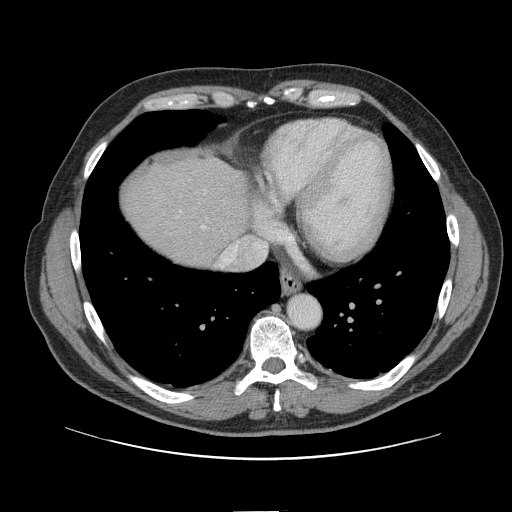
Contrast-enhanced abdominal CT, one axial slice; slice 136 of 161 in the series (ordered by position); 120 kVp; intravenous contrast given; soft-tissue window (W 400 / L 40 HU); 2.5 mm slice thickness; 512 × 512 image matrix. Male patient, age 66 years. Case-level facts recorded for this patient, not image findings: diagnosis: colorectal cancer liver metastases, imaged before liver resection; multiple liver metastases: no; largest metastasis: 3.5 cm; disease in both lobes: no.
Annotated regions visible in this slice (expert manual segmentation):
- hepatic veins: box from (x=203, y=192) to (x=241, y=268) px
- liver: (x=124, y=162)–(x=248, y=266)
- planned liver remnant (the part of the liver to remain after resection): (x=124, y=162)–(x=248, y=266)